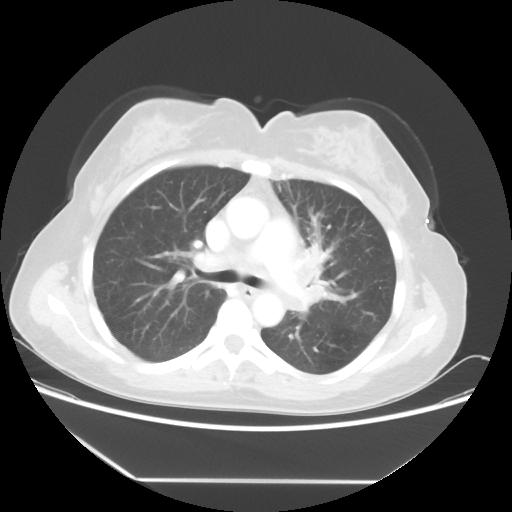
Chest CT, one axial slice. Slice 33 of 52 in the series (ordered by position). Lung window (W 1500 / L -600 HU). 5 mm slice thickness. 512 × 512 image matrix, field of view 390 × 390 mm. Female patient, age 50 years. From the clinical record (not read from this slice): clinical TNM (as recorded): T2 N3 M0.
Annotated regions visible in this slice (rectangle marked by the reading radiologist):
- lung tumour (recorded histology: adenocarcinoma): bounding box [x1, y1, x2, y2] px = [295, 224, 355, 324]